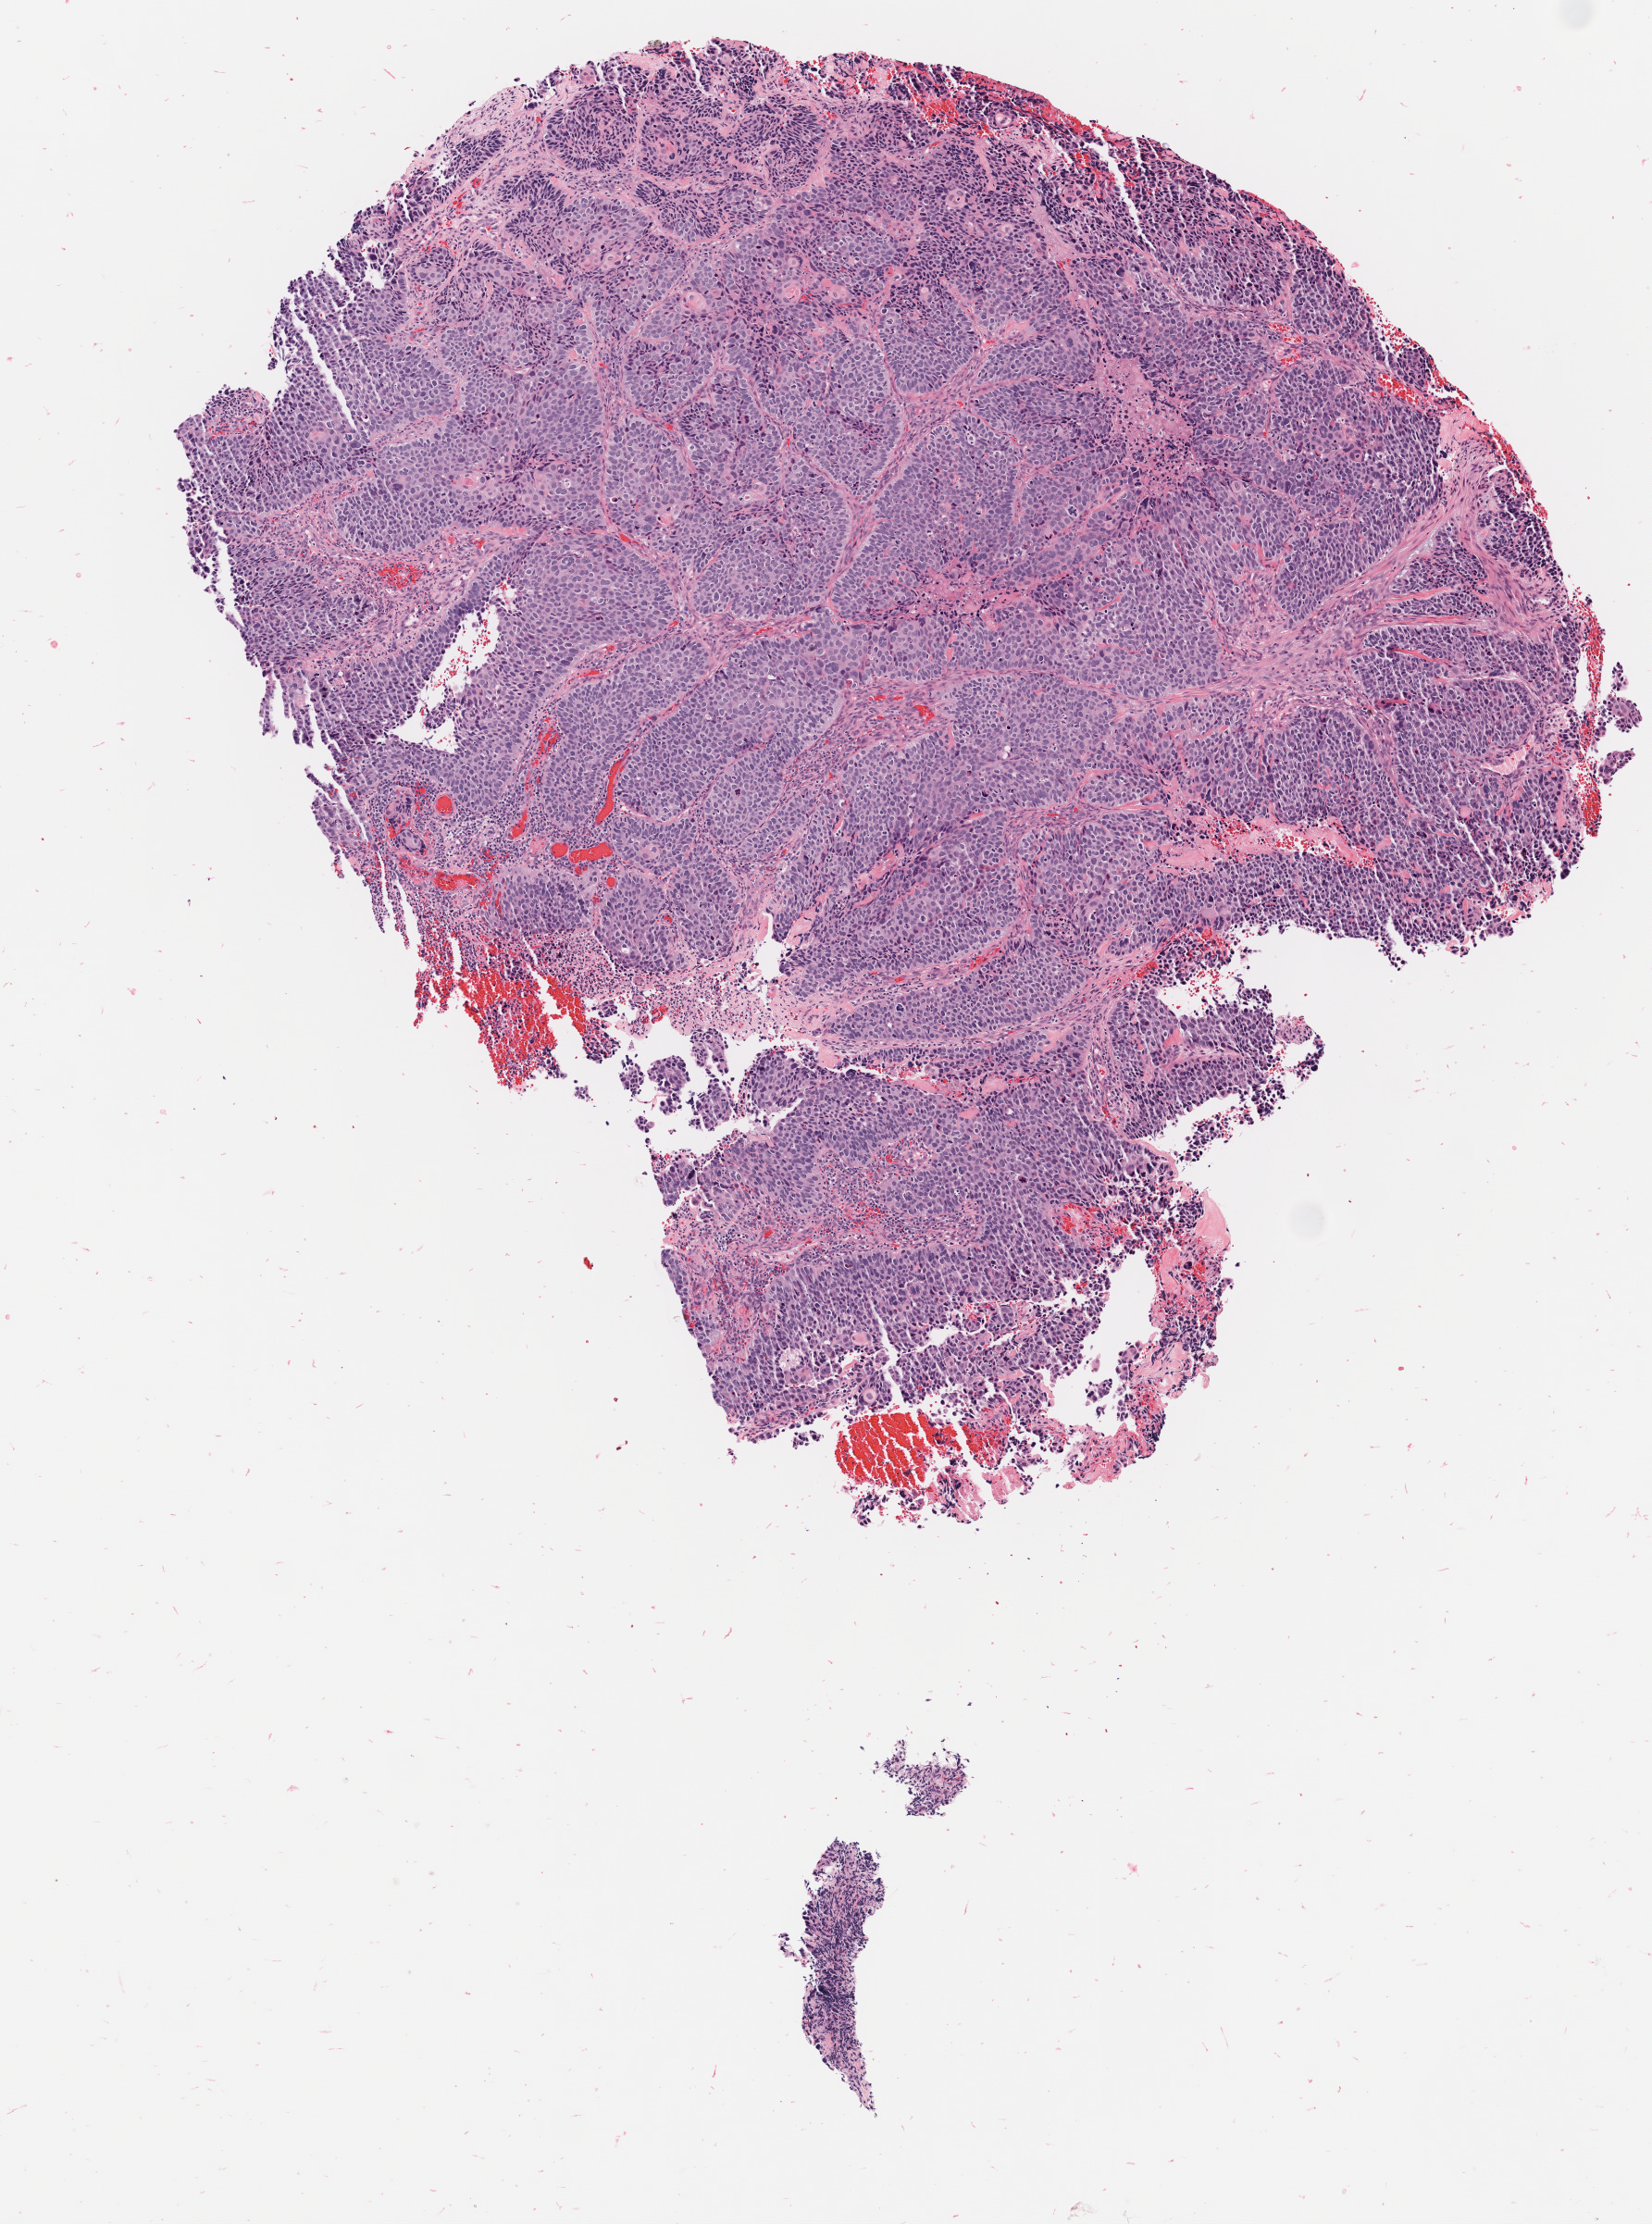
Whole-slide image, H&E stain, low-resolution overview of the scanned area, about 3.6 x 4.8 mm. Tumor tissue. Anatomic site: cervix. Female patient, aged 58.
Histologic diagnosis: Squamous cell carcinoma, large cell, nonkeratinizing, NOS.